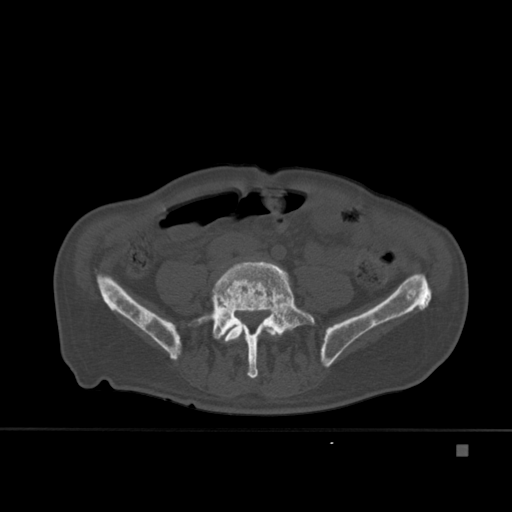
CT including the spine, one axial slice. Position 108 of 451 along the scan axis. Bone window (W 1800 / L 400 HU). 1.5 mm slice thickness. 512 × 512 image matrix. Patient: male, 75 years. Case-level facts recorded for this patient, not image findings: primary cancer: prostate.
Outlined on this slice (semi-automatically segmented with operator editing):
- L4 vertebra: bounding box (x1, y1, x2, y2) in pixels: (224, 324, 278, 378)
- L5 vertebra: (189, 261, 315, 379)
- T7 vertebra: (265, 314, 274, 325)